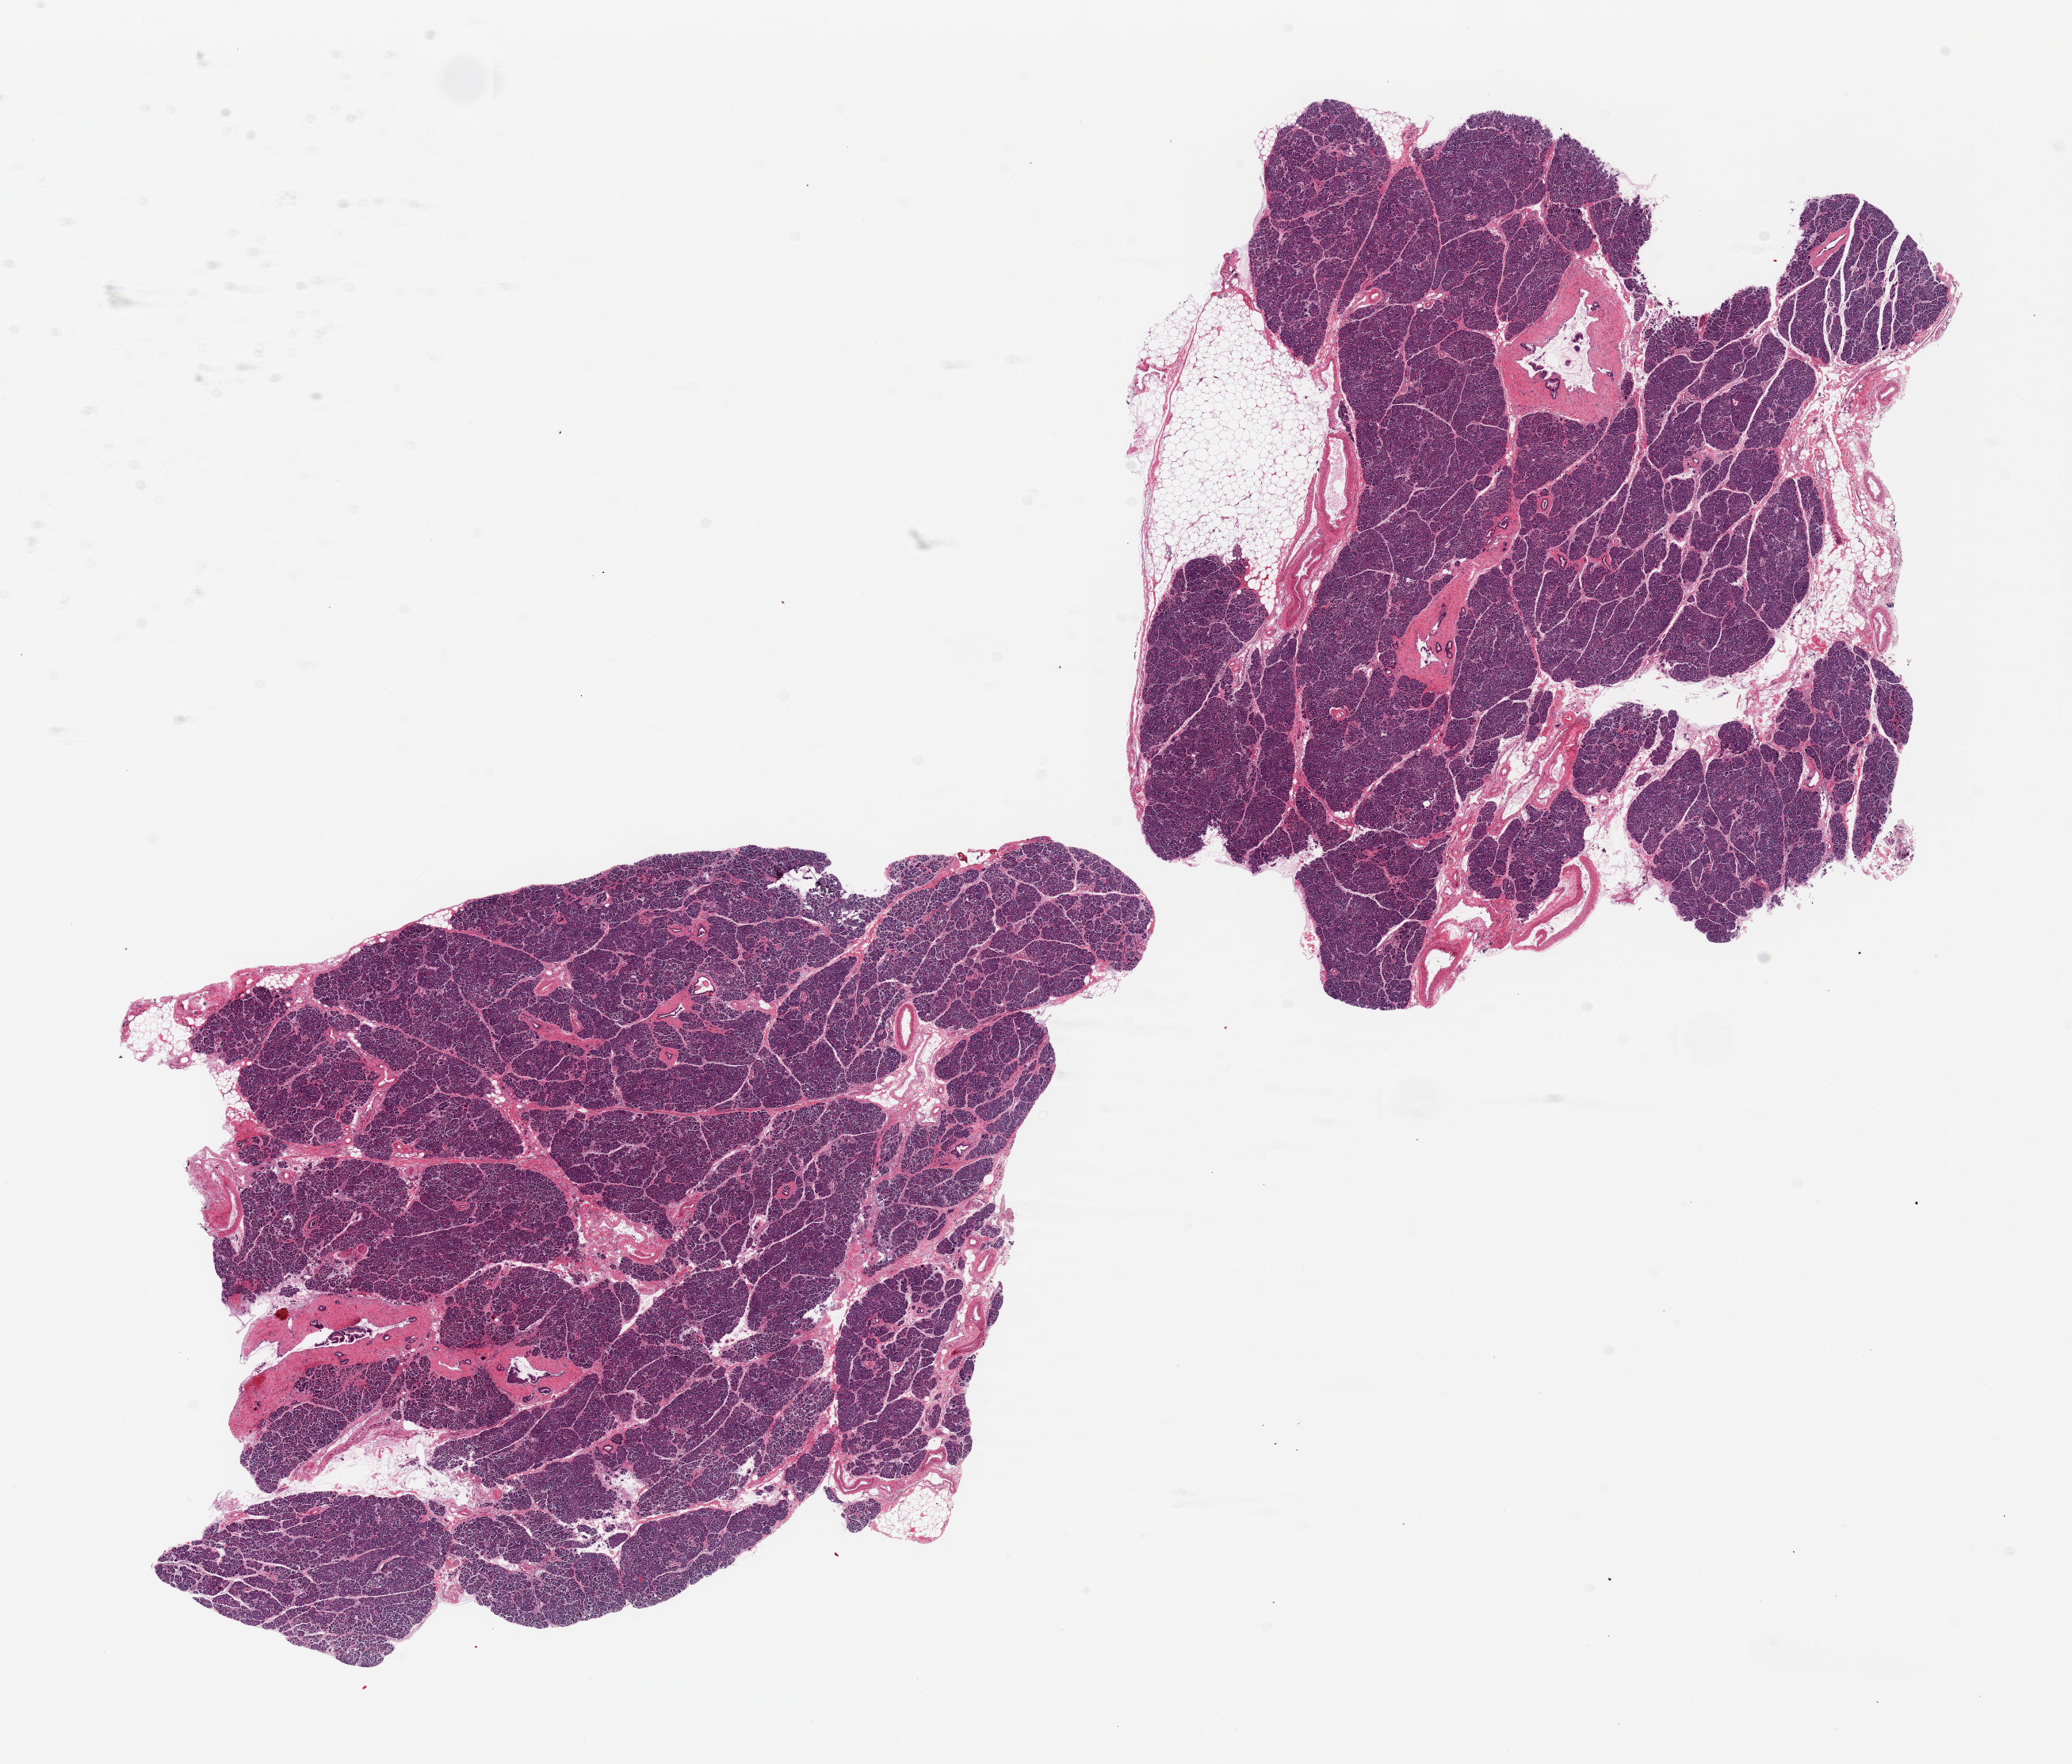
Whole-slide image, hematoxylin and eosin (H&E) stain, a low-resolution overview of the entire scanned area, about 20.7 x 17.6 mm. PAXgene-fixed paraffin-embedded (PFPE) section. Target tissue: pancreas. Donor tissue sample. Donor sex: male.
Review note (as recorded): 2 pieces ~8x7mm, well preserved, miniaml adherhent fat, Islets not prominent.